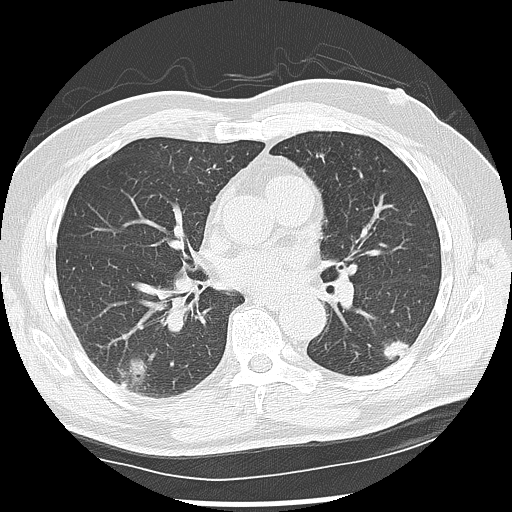
Low-dose screening chest CT, one axial slice. Position 65 of 142 along the scan axis. Reconstruction kernel LUNG. 120 kVp. Lung window (W 1500 / L -600 HU). 512 × 512 image matrix, field of view 360 × 360 mm.
Outlined on this slice (manually delineated by an expert):
- lesion 1 (nodule, lower lobe of left lung): bounding box <384,340,409,360> (left, top, right, bottom; pixels)
- lesion 2 (nodule, lower lobe of right lung): <128,360,147,388>